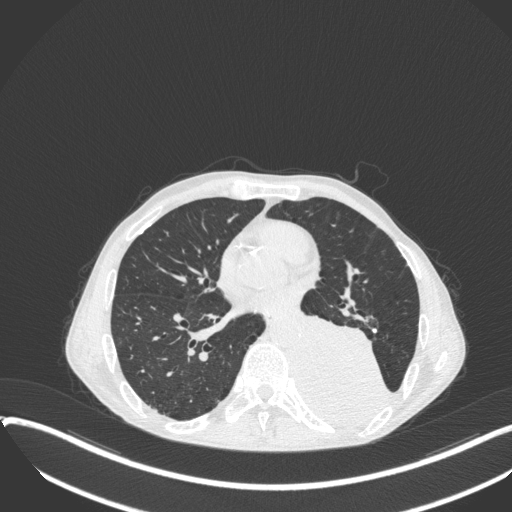
Chest CT, one axial slice; 120 kVp; lung window (W 1500 / L -600 HU); 1 mm slice thickness; 512 × 512 image matrix, field of view 400 × 400 mm. Patient: male, 57 years. From the clinical record (not read from this slice): clinical TNM (as recorded): T4 N0 M0.
Annotated regions visible in this slice (bounding box drawn by a radiologist):
- lung tumour (recorded histology: squamous cell carcinoma): bounding box (x1, y1, x2, y2) in pixels: (298, 311, 394, 428)